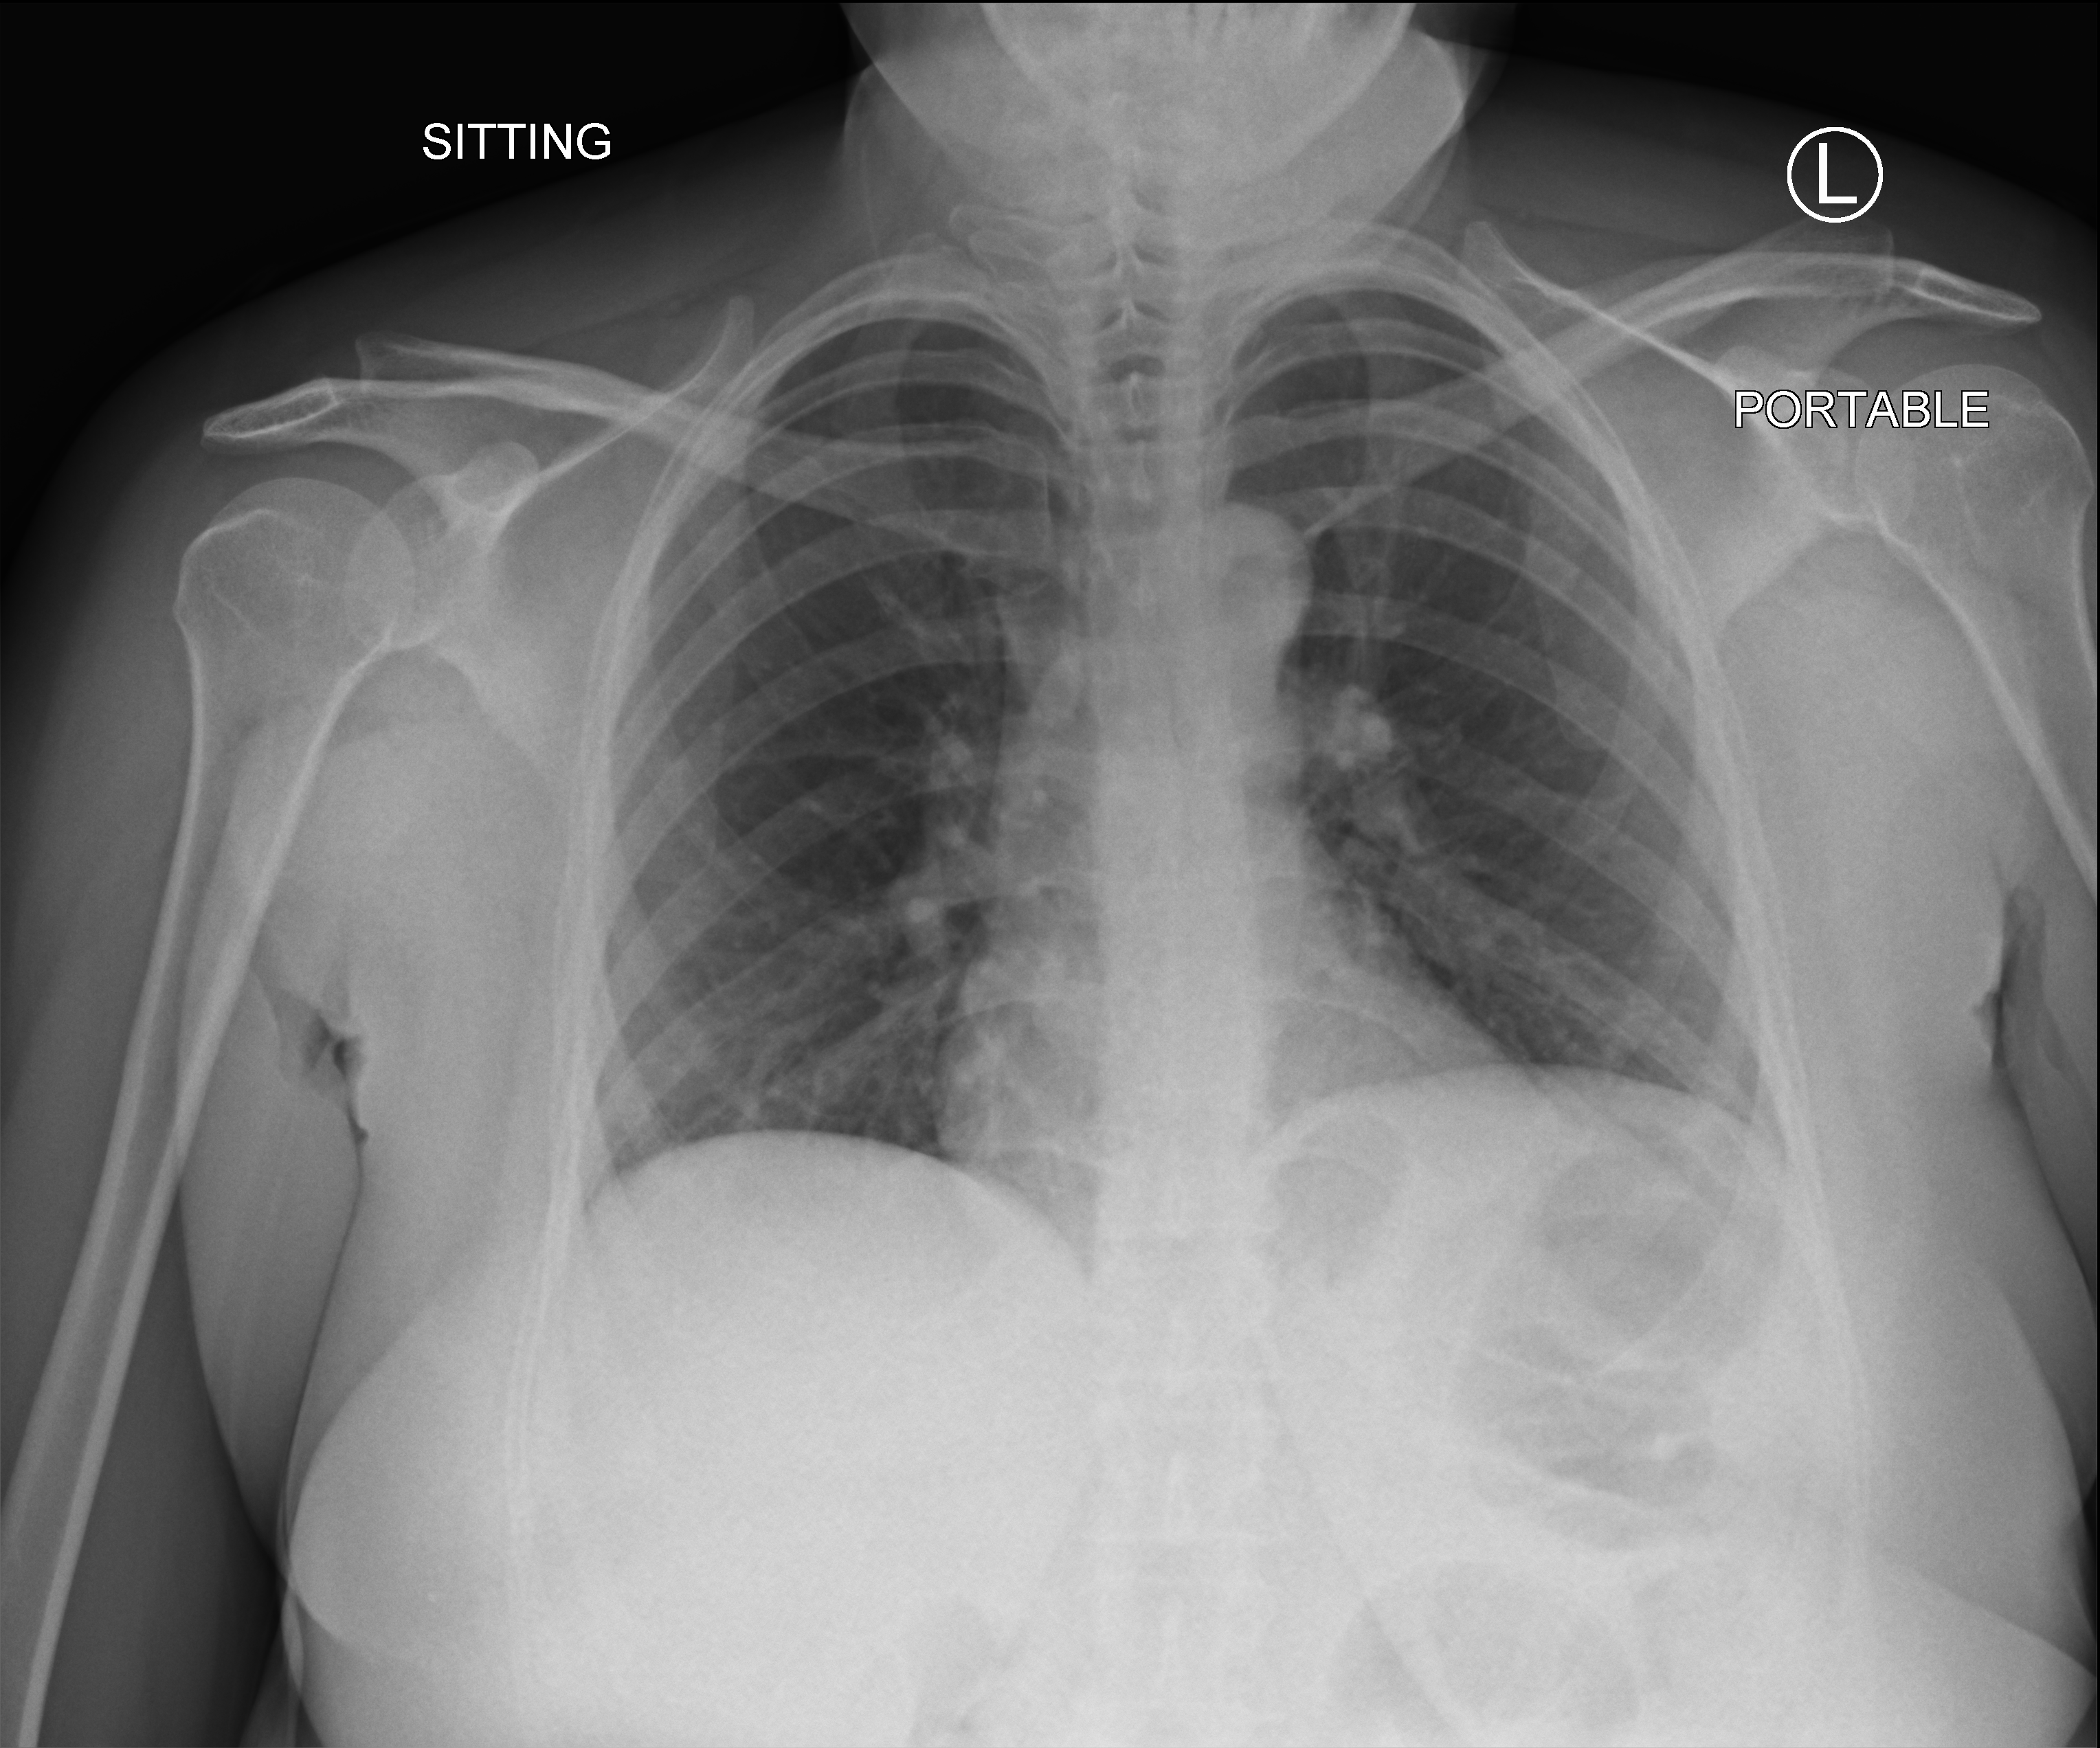
Portable chest radiograph, anteroposterior (AP) projection. Patient hospitalised with COVID-19; female, aged 18–59 years.
Admission-level facts for this patient (not findings on this image; timing relative to this image not recorded):
- admitted to intensive care during this hospital stay: no
- diabetes (admission record): no
- mechanically ventilated during this hospital stay: no